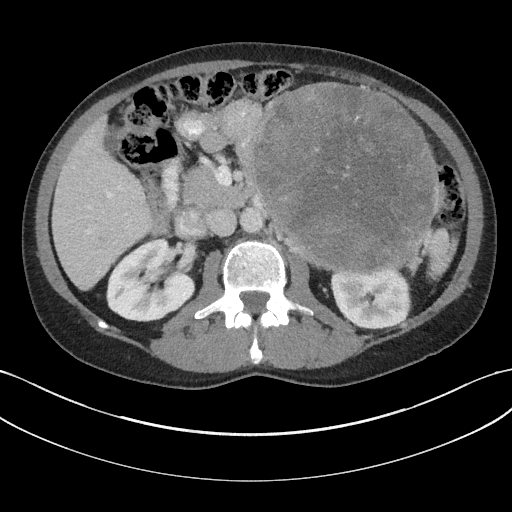
Contrast-enhanced abdominal CT, one axial slice; slice 98 of 147 in the series (ordered by position); reconstruction kernel I31f/3; intravenous contrast given; soft-tissue window (W 400 / L 40 HU); 3 mm slice thickness; 512 × 512 image matrix. Patient: male, 58 years. Case-level facts recorded for this patient, not image findings: diagnosis: adrenocortical carcinoma; tumour side: left adrenal; tumour size at pathology: 22 cm; Ki-67 index: 26 %; stage (as recorded): 2.
Outlined on this slice (semi-automatically segmented with operator editing):
- mass: bounding box (x1, y1, x2, y2) in pixels: (255, 84, 440, 271)